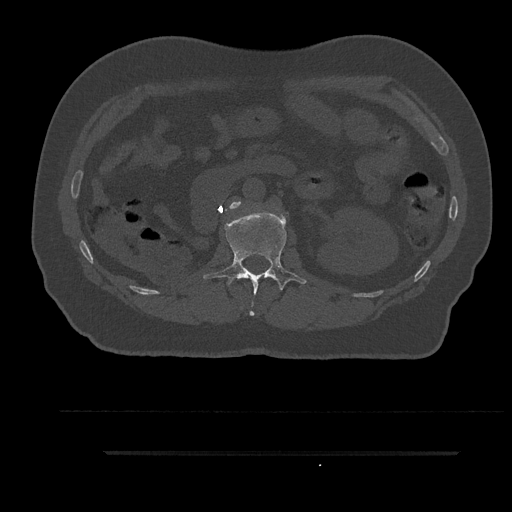
CT including the spine, one axial slice. Slice 171 of 797 in the series (ordered by position). 120 kVp. Bone window (W 1800 / L 400 HU). 0.5 mm slice thickness. 512 × 512 image matrix, field of view 432 × 432 mm. Patient: male, 63 years. Case-level facts recorded for this patient, not image findings: primary cancer: renal; vertebrae with lytic lesions (as recorded): T8.
Outlined on this slice (semi-automatic segmentation, software-assisted and operator-edited):
- L1 vertebra: bounding box (x1, y1, x2, y2) in pixels: (203, 211, 306, 316)
- L2 vertebra: (229, 201, 241, 209)